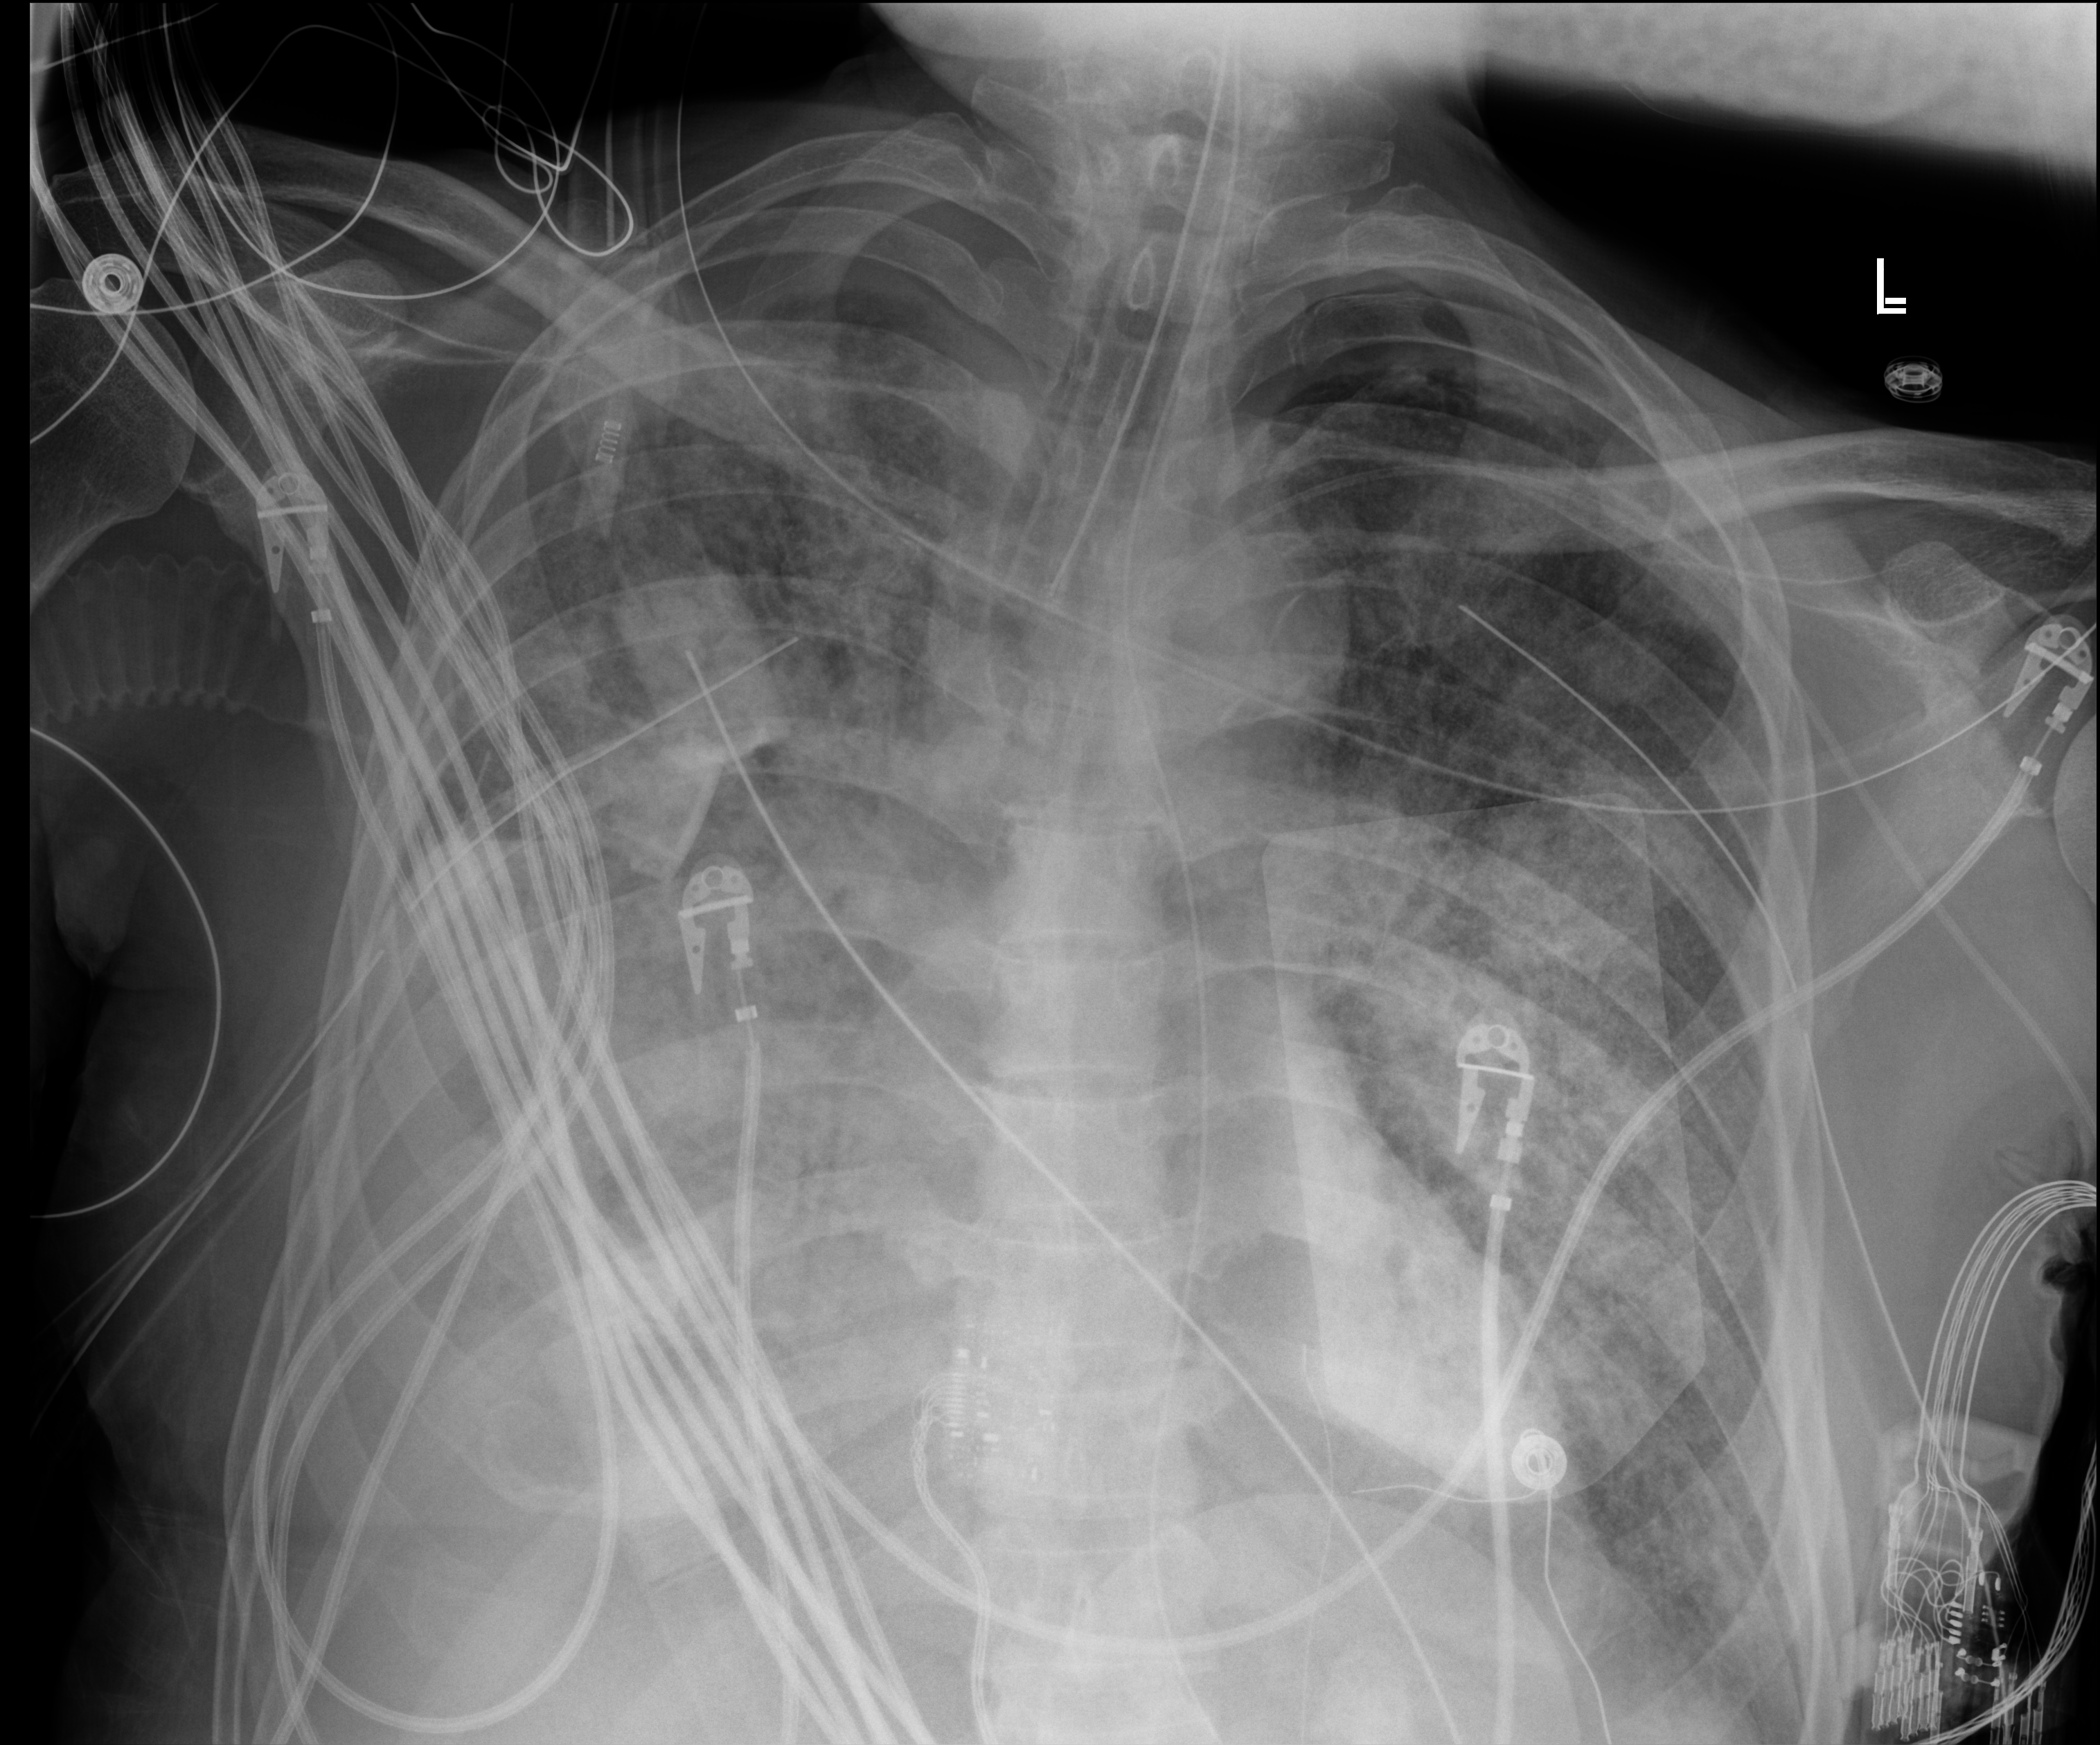
Portable chest radiograph; anteroposterior (AP) projection. Male patient hospitalised with COVID-19, age 60–74 years.
Hospital-stay facts (about this admission, not read from this image; timing relative to this image not recorded): mechanically ventilated during this hospital stay: yes.